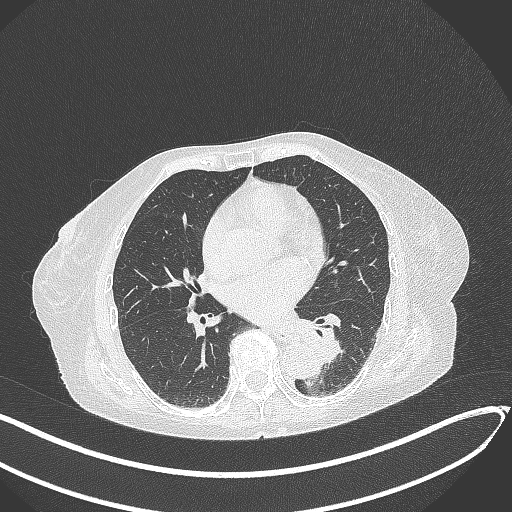
Chest CT, one axial slice; slice 115 of 324 in the series (ordered by position); reconstruction kernel B70f; 120 kVp; lung window (W 1500 / L -600 HU); 1 mm slice thickness; 512 × 512 image matrix. Female patient, age 82 years. Case-level facts recorded for this patient, not image findings: clinical TNM (as recorded): T1b N0 M1.
Outlined on this slice (bounding box drawn by a radiologist):
- lung tumour (recorded histology: adenocarcinoma): bounding box [x1, y1, x2, y2] px = [290, 314, 348, 364]